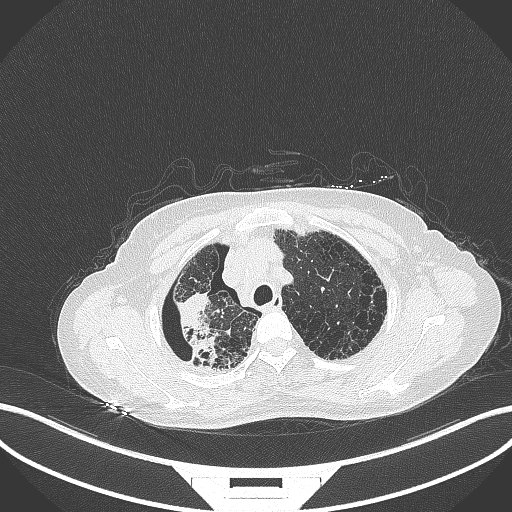
Chest CT, one axial slice; slice 292 of 408 in the series (ordered by position); reconstruction kernel B70f; 120 kVp; lung window (W 1500 / L -600 HU); 512 × 512 image matrix. Patient: female, 64 years. Case-level facts recorded for this patient, not image findings: clinical TNM (as recorded): T3 N3 M0.
Outlined on this slice (bounding box drawn by a radiologist):
- lung tumour (recorded histology: squamous cell carcinoma): box from (x=173, y=292) to (x=219, y=368) px